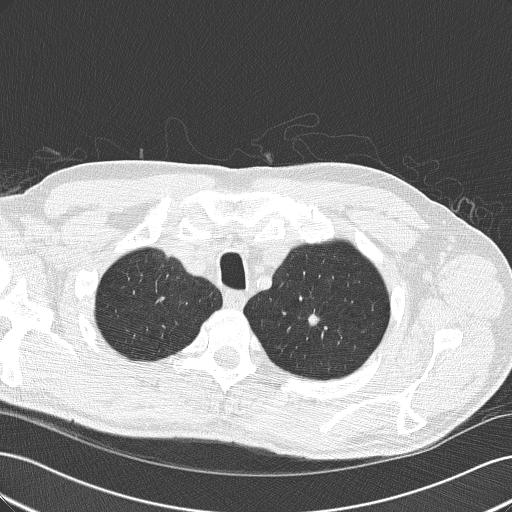
Low-dose screening chest CT, one axial slice. Slice 157 of 189 in the series (ordered by position). One of 2 acquisitions stored at this slice position. Lung window (W 1500 / L -600 HU). 2 mm slice thickness. 512 × 512 image matrix, field of view 360 × 360 mm.
Structures marked on this image (manually delineated by an expert):
- lesion 1 (tumor, upper lobe of left lung): bounding box <308,310,326,329> (left, top, right, bottom; pixels)